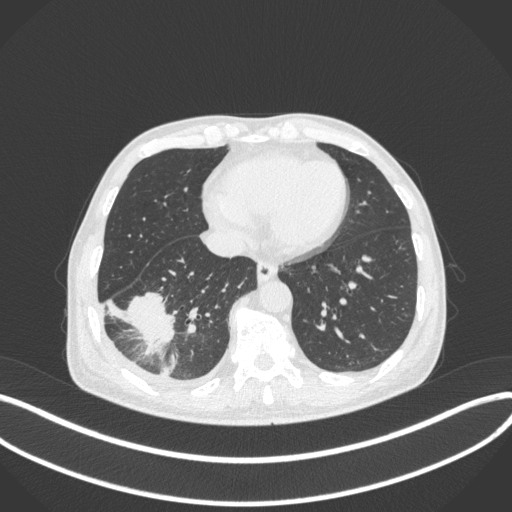
Chest CT, one axial slice; position 116 of 385 along the scan axis; reconstruction kernel B31f; lung window (W 1500 / L -600 HU); 512 × 512 image matrix, field of view 400 × 400 mm. Male patient, age 64 years. From the clinical record (not read from this slice): clinical TNM (as recorded): T3 N0 M0; histopathological grade: G2-3.
Annotated regions visible in this slice (rectangle marked by the reading radiologist):
- lung tumour (recorded histology: adenocarcinoma): bounding box [x1, y1, x2, y2] px = [123, 286, 178, 358]